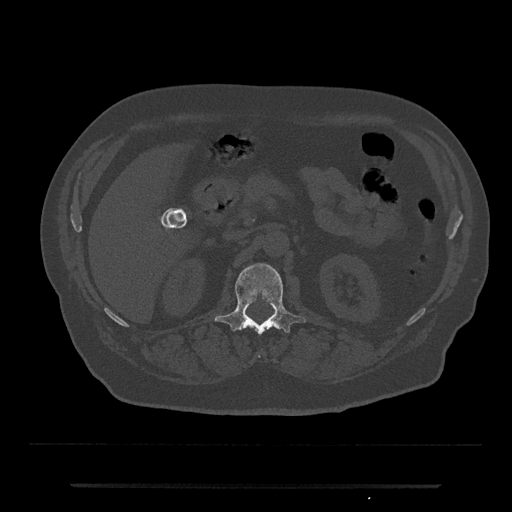
CT including the spine, one axial slice; position 540 of 797 along the scan axis; reconstruction kernel Br40s/3; 120 kVp; bone window (W 1800 / L 400 HU); 512 × 512 image matrix, field of view 434 × 434 mm. Patient: male, 80 years. Case-level facts recorded for this patient, not image findings: primary cancer: prostate; vertebrae with lytic lesions (as recorded): L1, T11.
Outlined on this slice (semi-automatic segmentation, software-assisted and operator-edited):
- L1 vertebra: bounding box <214,263,306,357> (left, top, right, bottom; pixels)